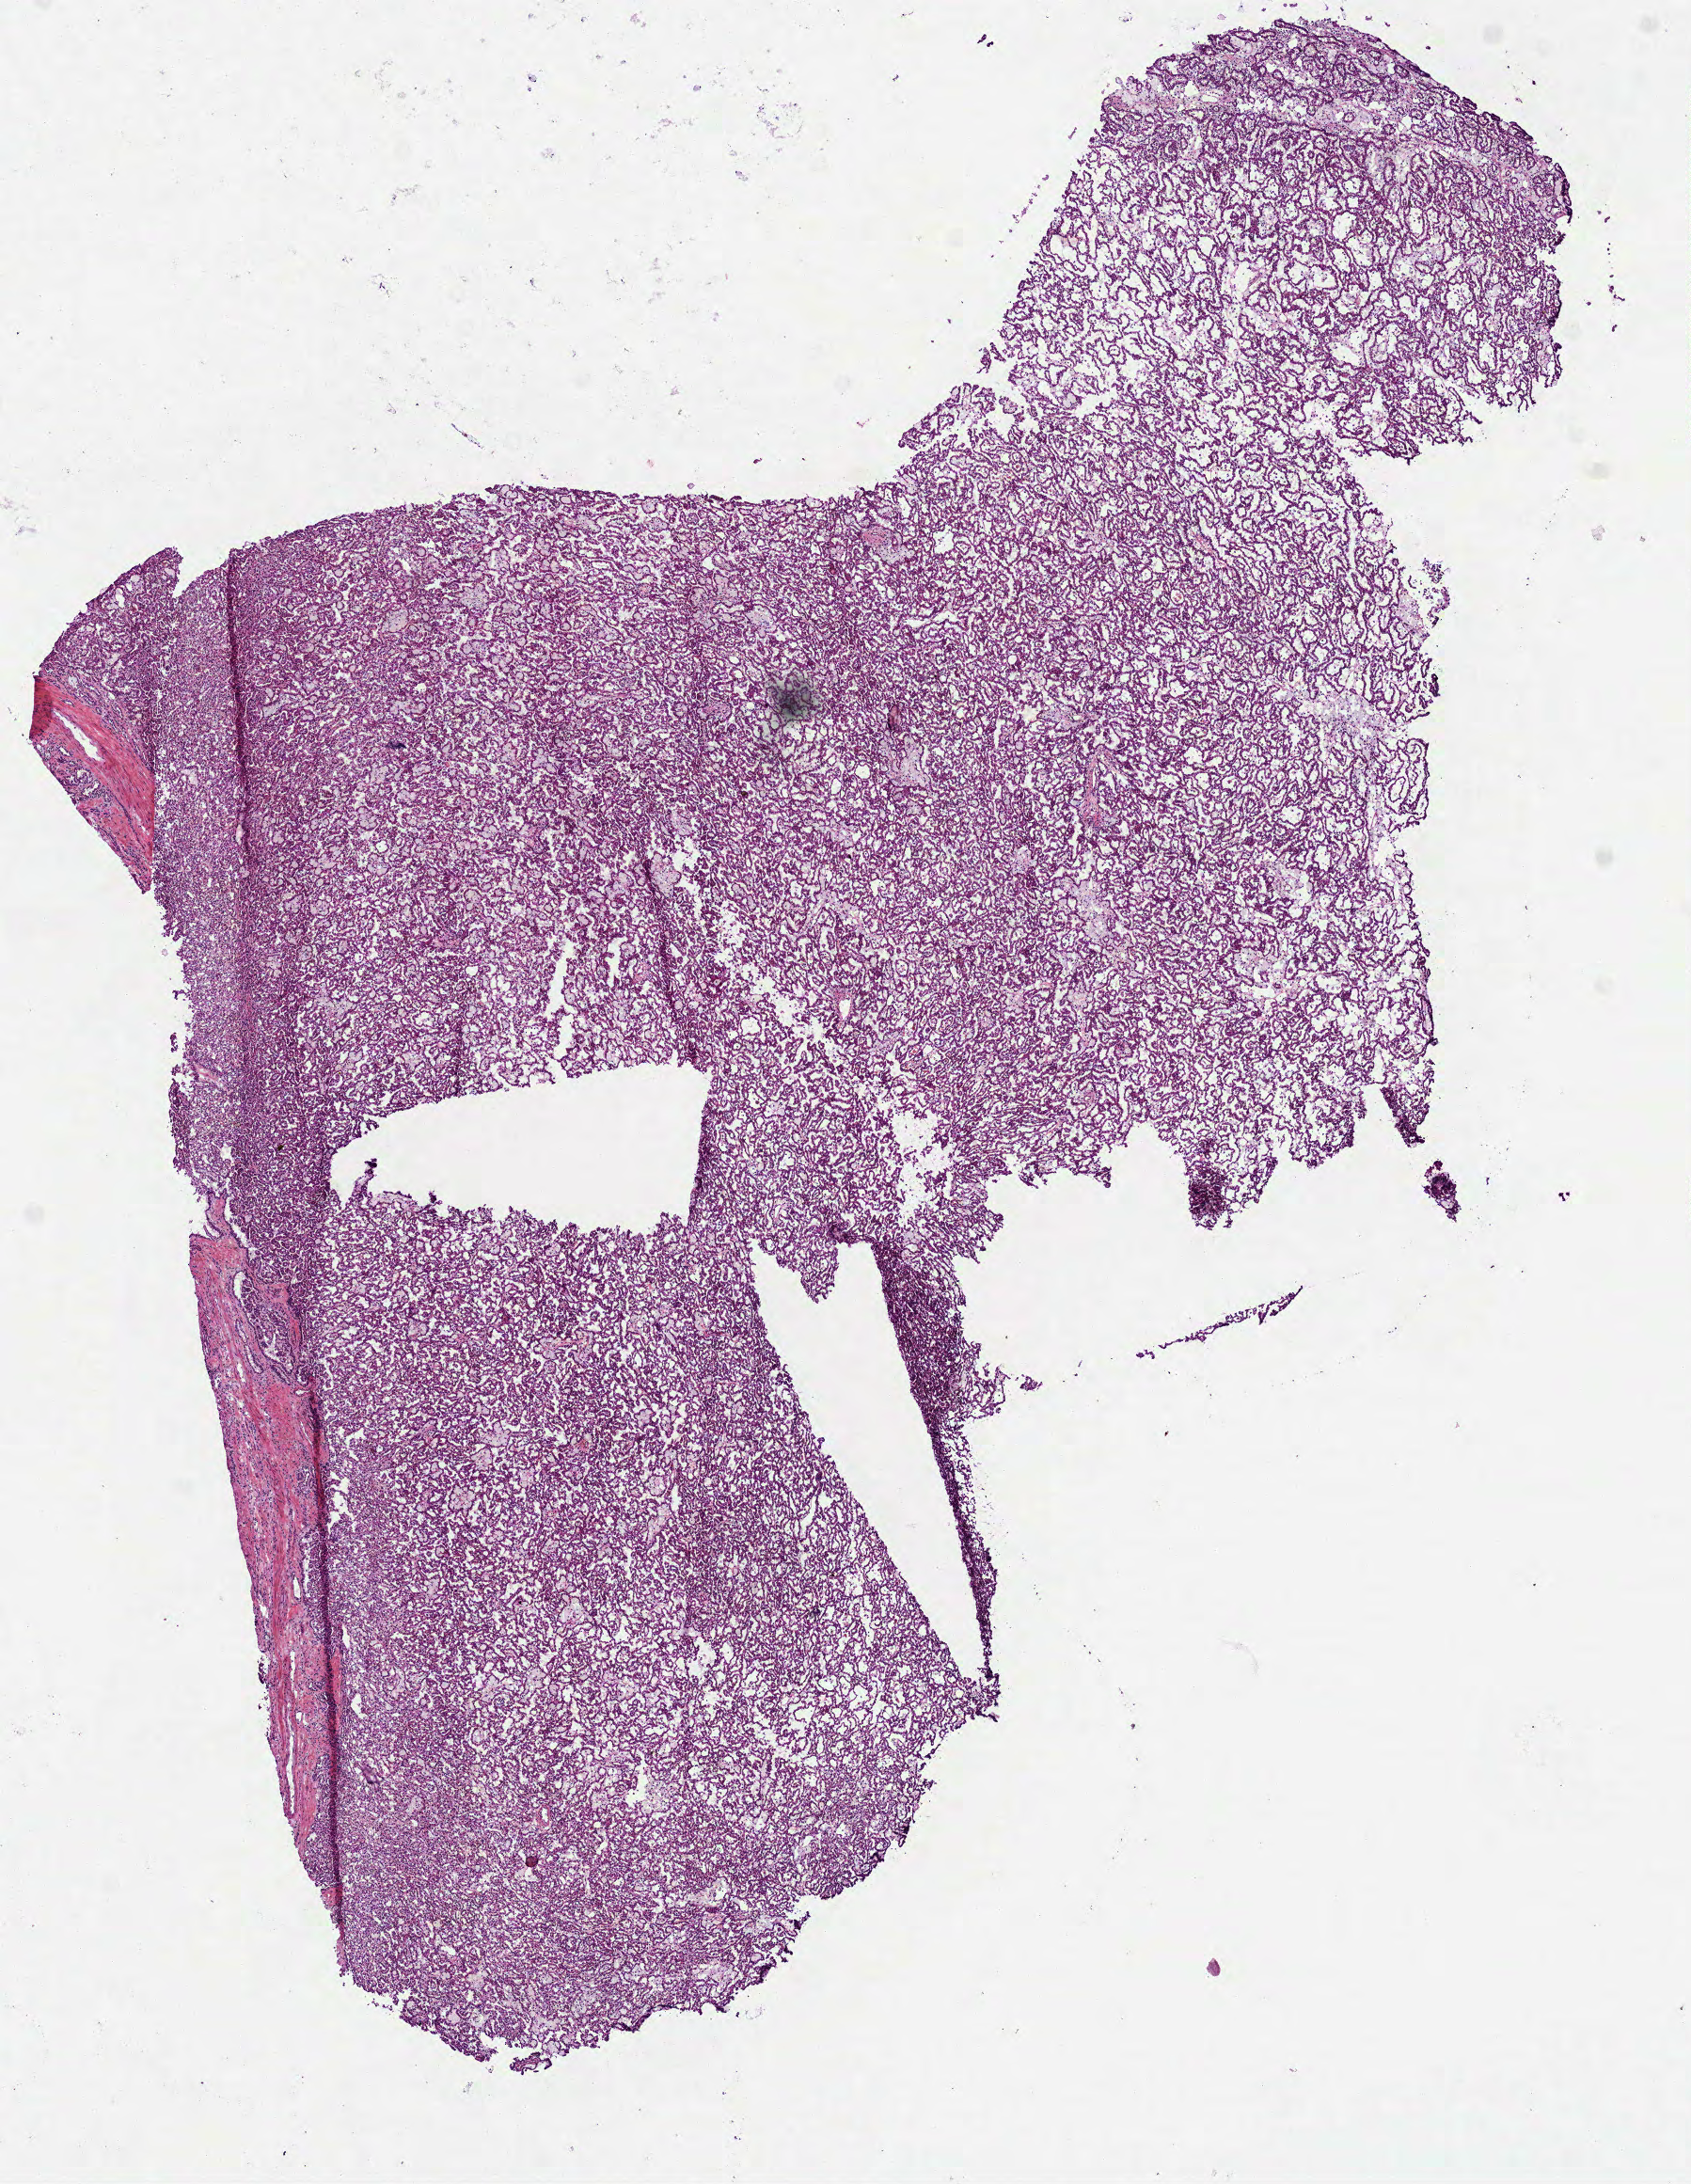
Digitized H&E-stained tissue section (whole slide), shown as a low-resolution overview of the whole scanned area (about 7.3 x 9.4 mm, slide scanned at 40x); frozen section from the bottom of the tissue portion; primary tumour sample from the kidney. Male patient; age at initial diagnosis 43 years. Pathologist review of this section (percent, as recorded): tumour cells 100%, tumour nuclei 80%, normal cells 0%, stromal cells 0%, necrosis 0%. Inflammatory infiltration, as recorded: lymphocyte infiltration 0%, monocyte infiltration 15%, neutrophil infiltration 0%.
Histologic diagnosis: Papillary adenocarcinoma, NOS. AJCC pathologic stage: I (6th edition). Laterality: right.